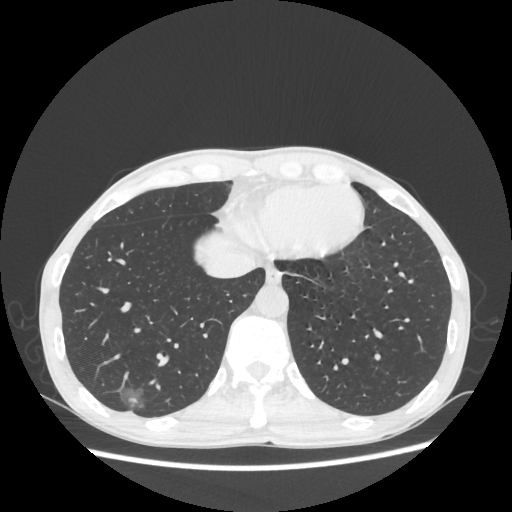
Chest CT, one axial slice; slice 71 of 270 in the series (ordered by position); reconstruction kernel STANDARD; 100 kVp; lung window (W 1500 / L -600 HU); 512 × 512 image matrix. Patient: male, 60 years. Case-level facts recorded for this patient, not image findings: clinical TNM (as recorded): T1c N0 M0.
Structures marked on this image (rectangle marked by the reading radiologist):
- lung tumour (recorded histology: adenocarcinoma): box from (x=111, y=383) to (x=156, y=422) px